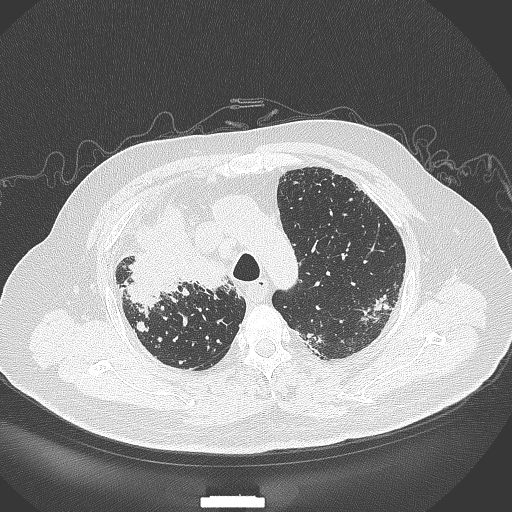
Chest CT, one axial slice. Position 275 of 384 along the scan axis. Reconstruction kernel B70f. 120 kVp. Lung window (W 1500 / L -600 HU). 1 mm slice thickness. 512 × 512 image matrix. Male patient, age 69 years. Case-level facts recorded for this patient, not image findings: clinical TNM (as recorded): T4 N3 M1.
Structures marked on this image (bounding box drawn by a radiologist):
- lung tumour (recorded histology: adenocarcinoma): bounding box [x1, y1, x2, y2] px = [119, 208, 226, 310]